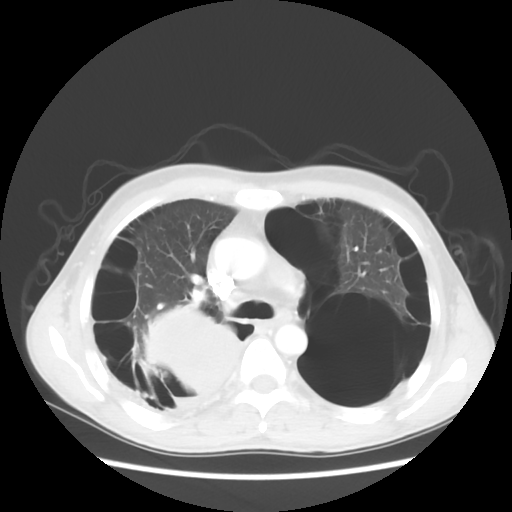
Chest CT, one axial slice. Slice 36 of 56 in the series (ordered by position). Lung window (W 1500 / L -600 HU). 512 × 512 image matrix, field of view 351 × 351 mm. Patient: male, 41 years. From the clinical record (not read from this slice): clinical TNM (as recorded): T4 N0 M1a; histopathological grade: G3.
Annotated regions visible in this slice (rectangle marked by the reading radiologist):
- lung tumour (recorded histology: large cell carcinoma): bounding box [x1, y1, x2, y2] px = [139, 298, 246, 410]